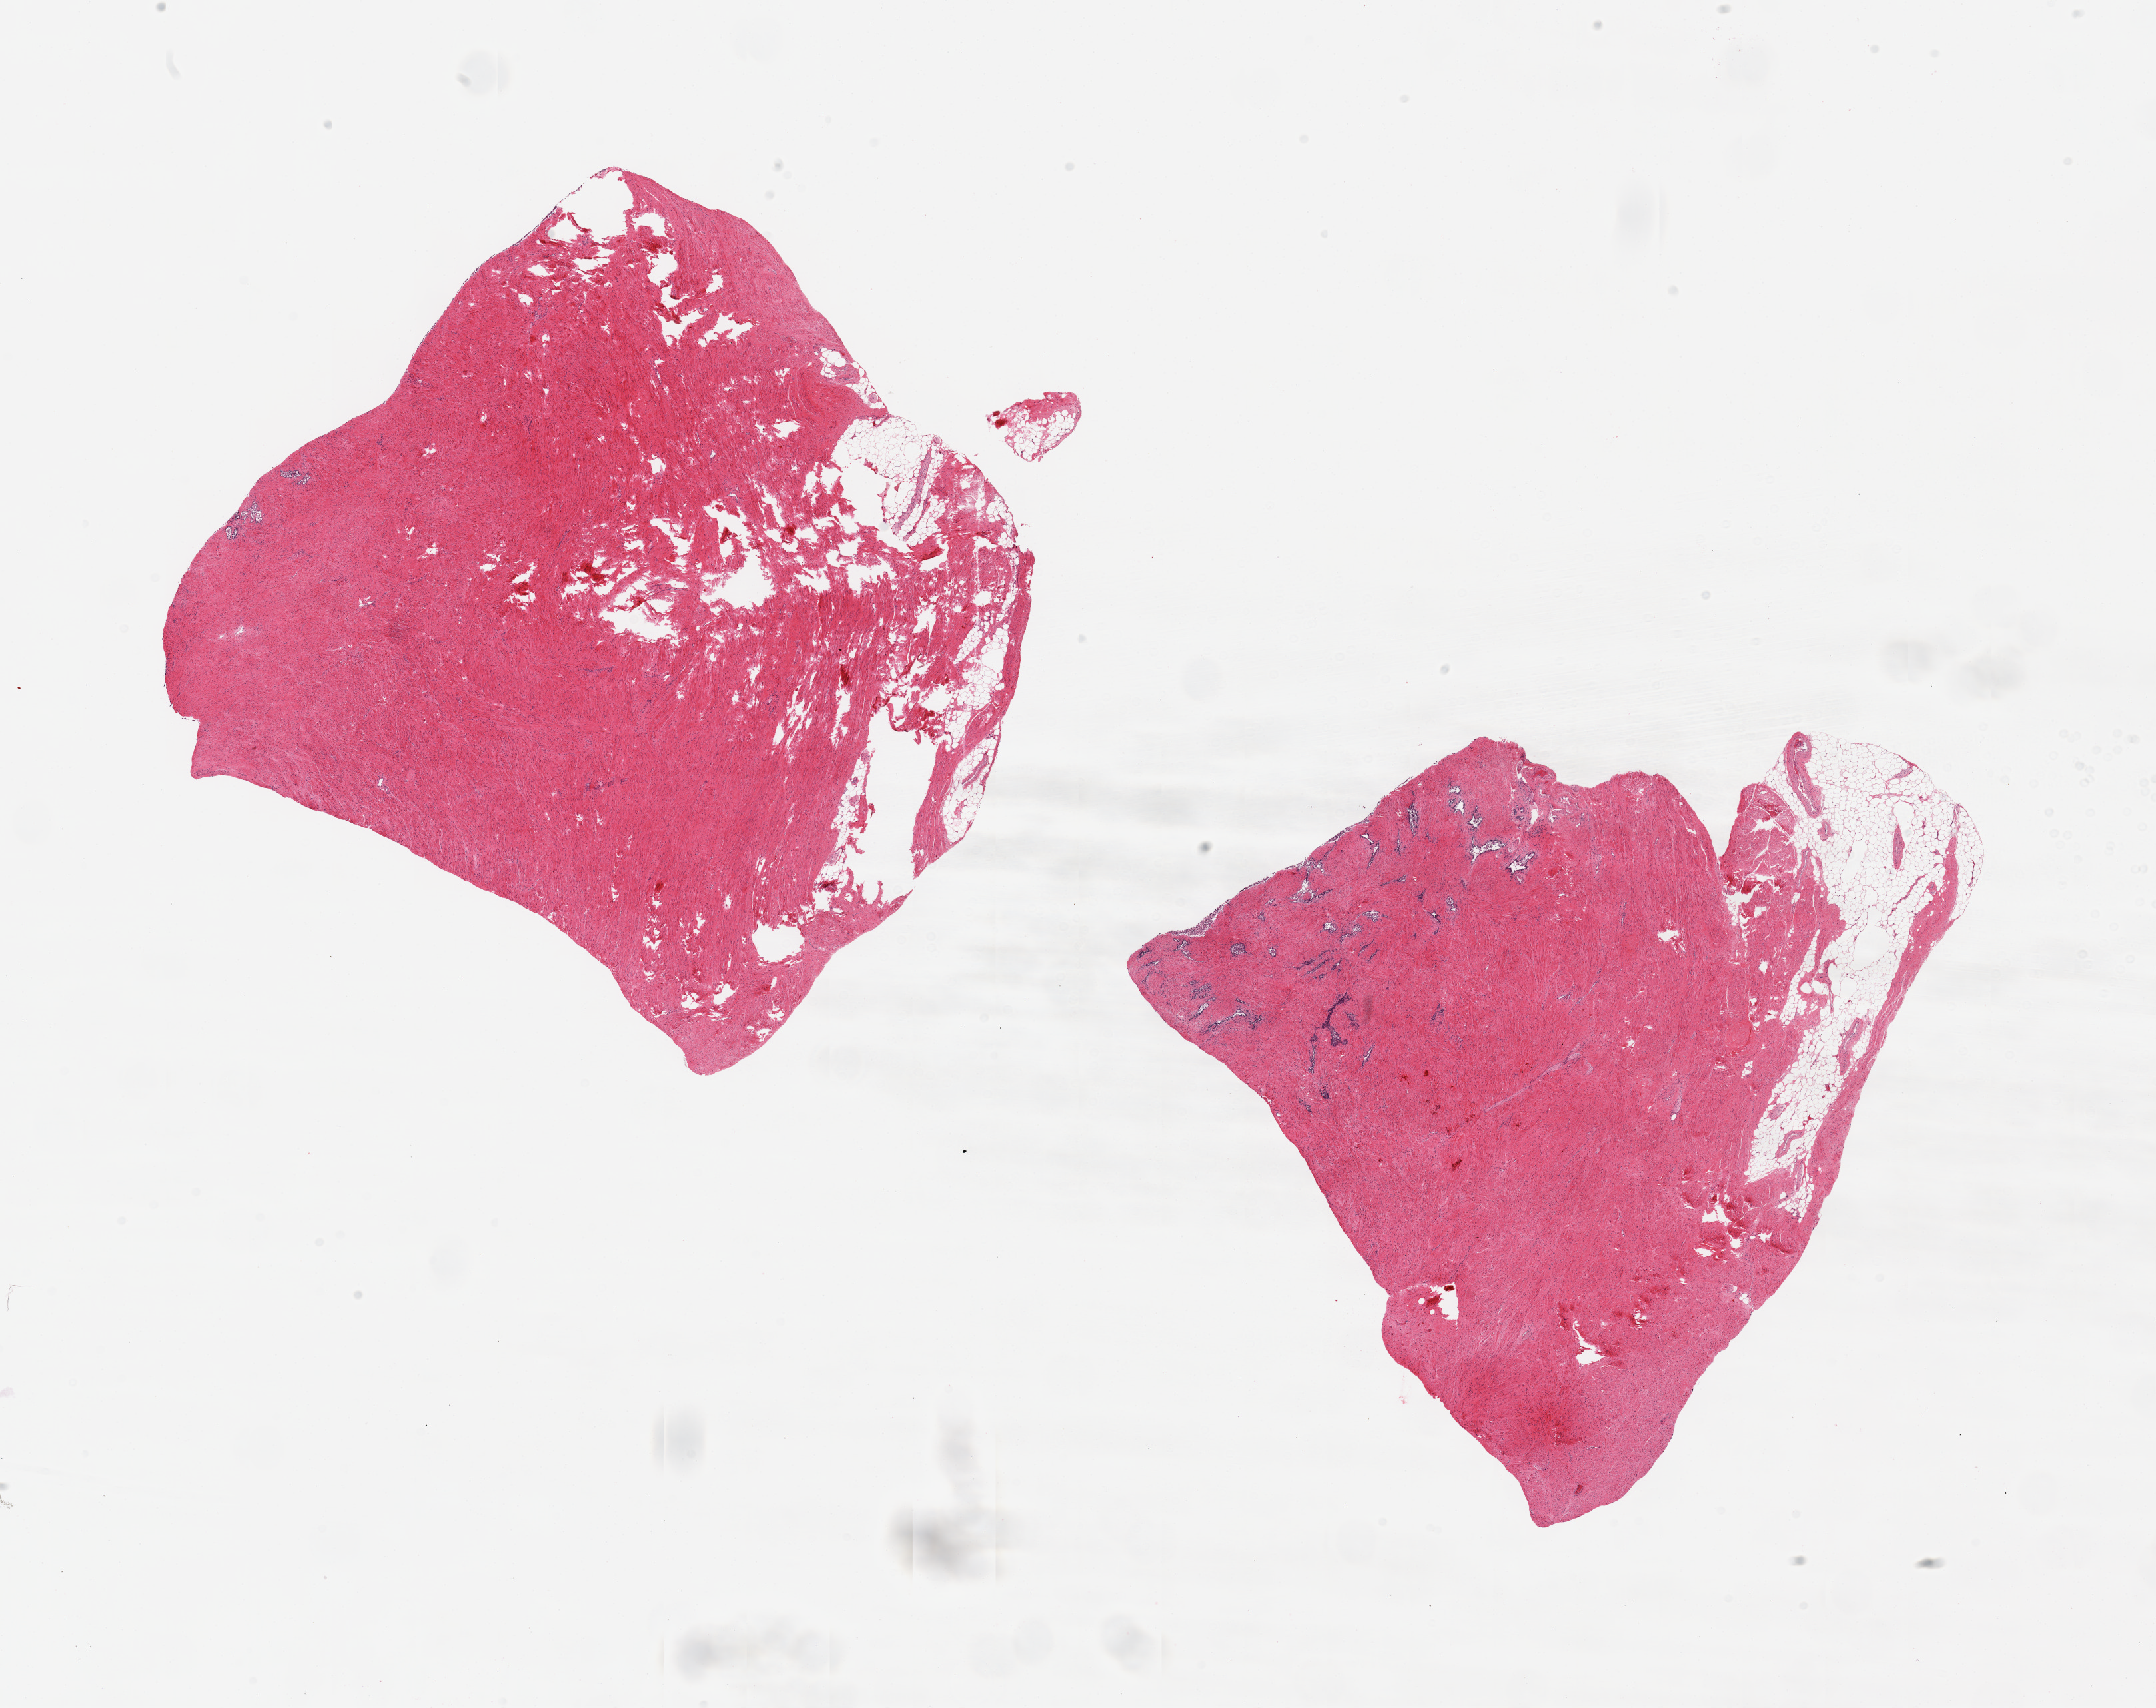
Whole-slide image, H&E stain, brightfield, shown as a low-resolution overview of the whole scanned area (about 25.6 x 20.3 mm); PAXgene-fixed paraffin-embedded (PFPE) section; section of prostate (target tissue); donor tissue sample. Donor: male.
• review note (as recorded): 2 pieces; mostly fibromuscular stroma with limited glandular component; sloughed epithelium